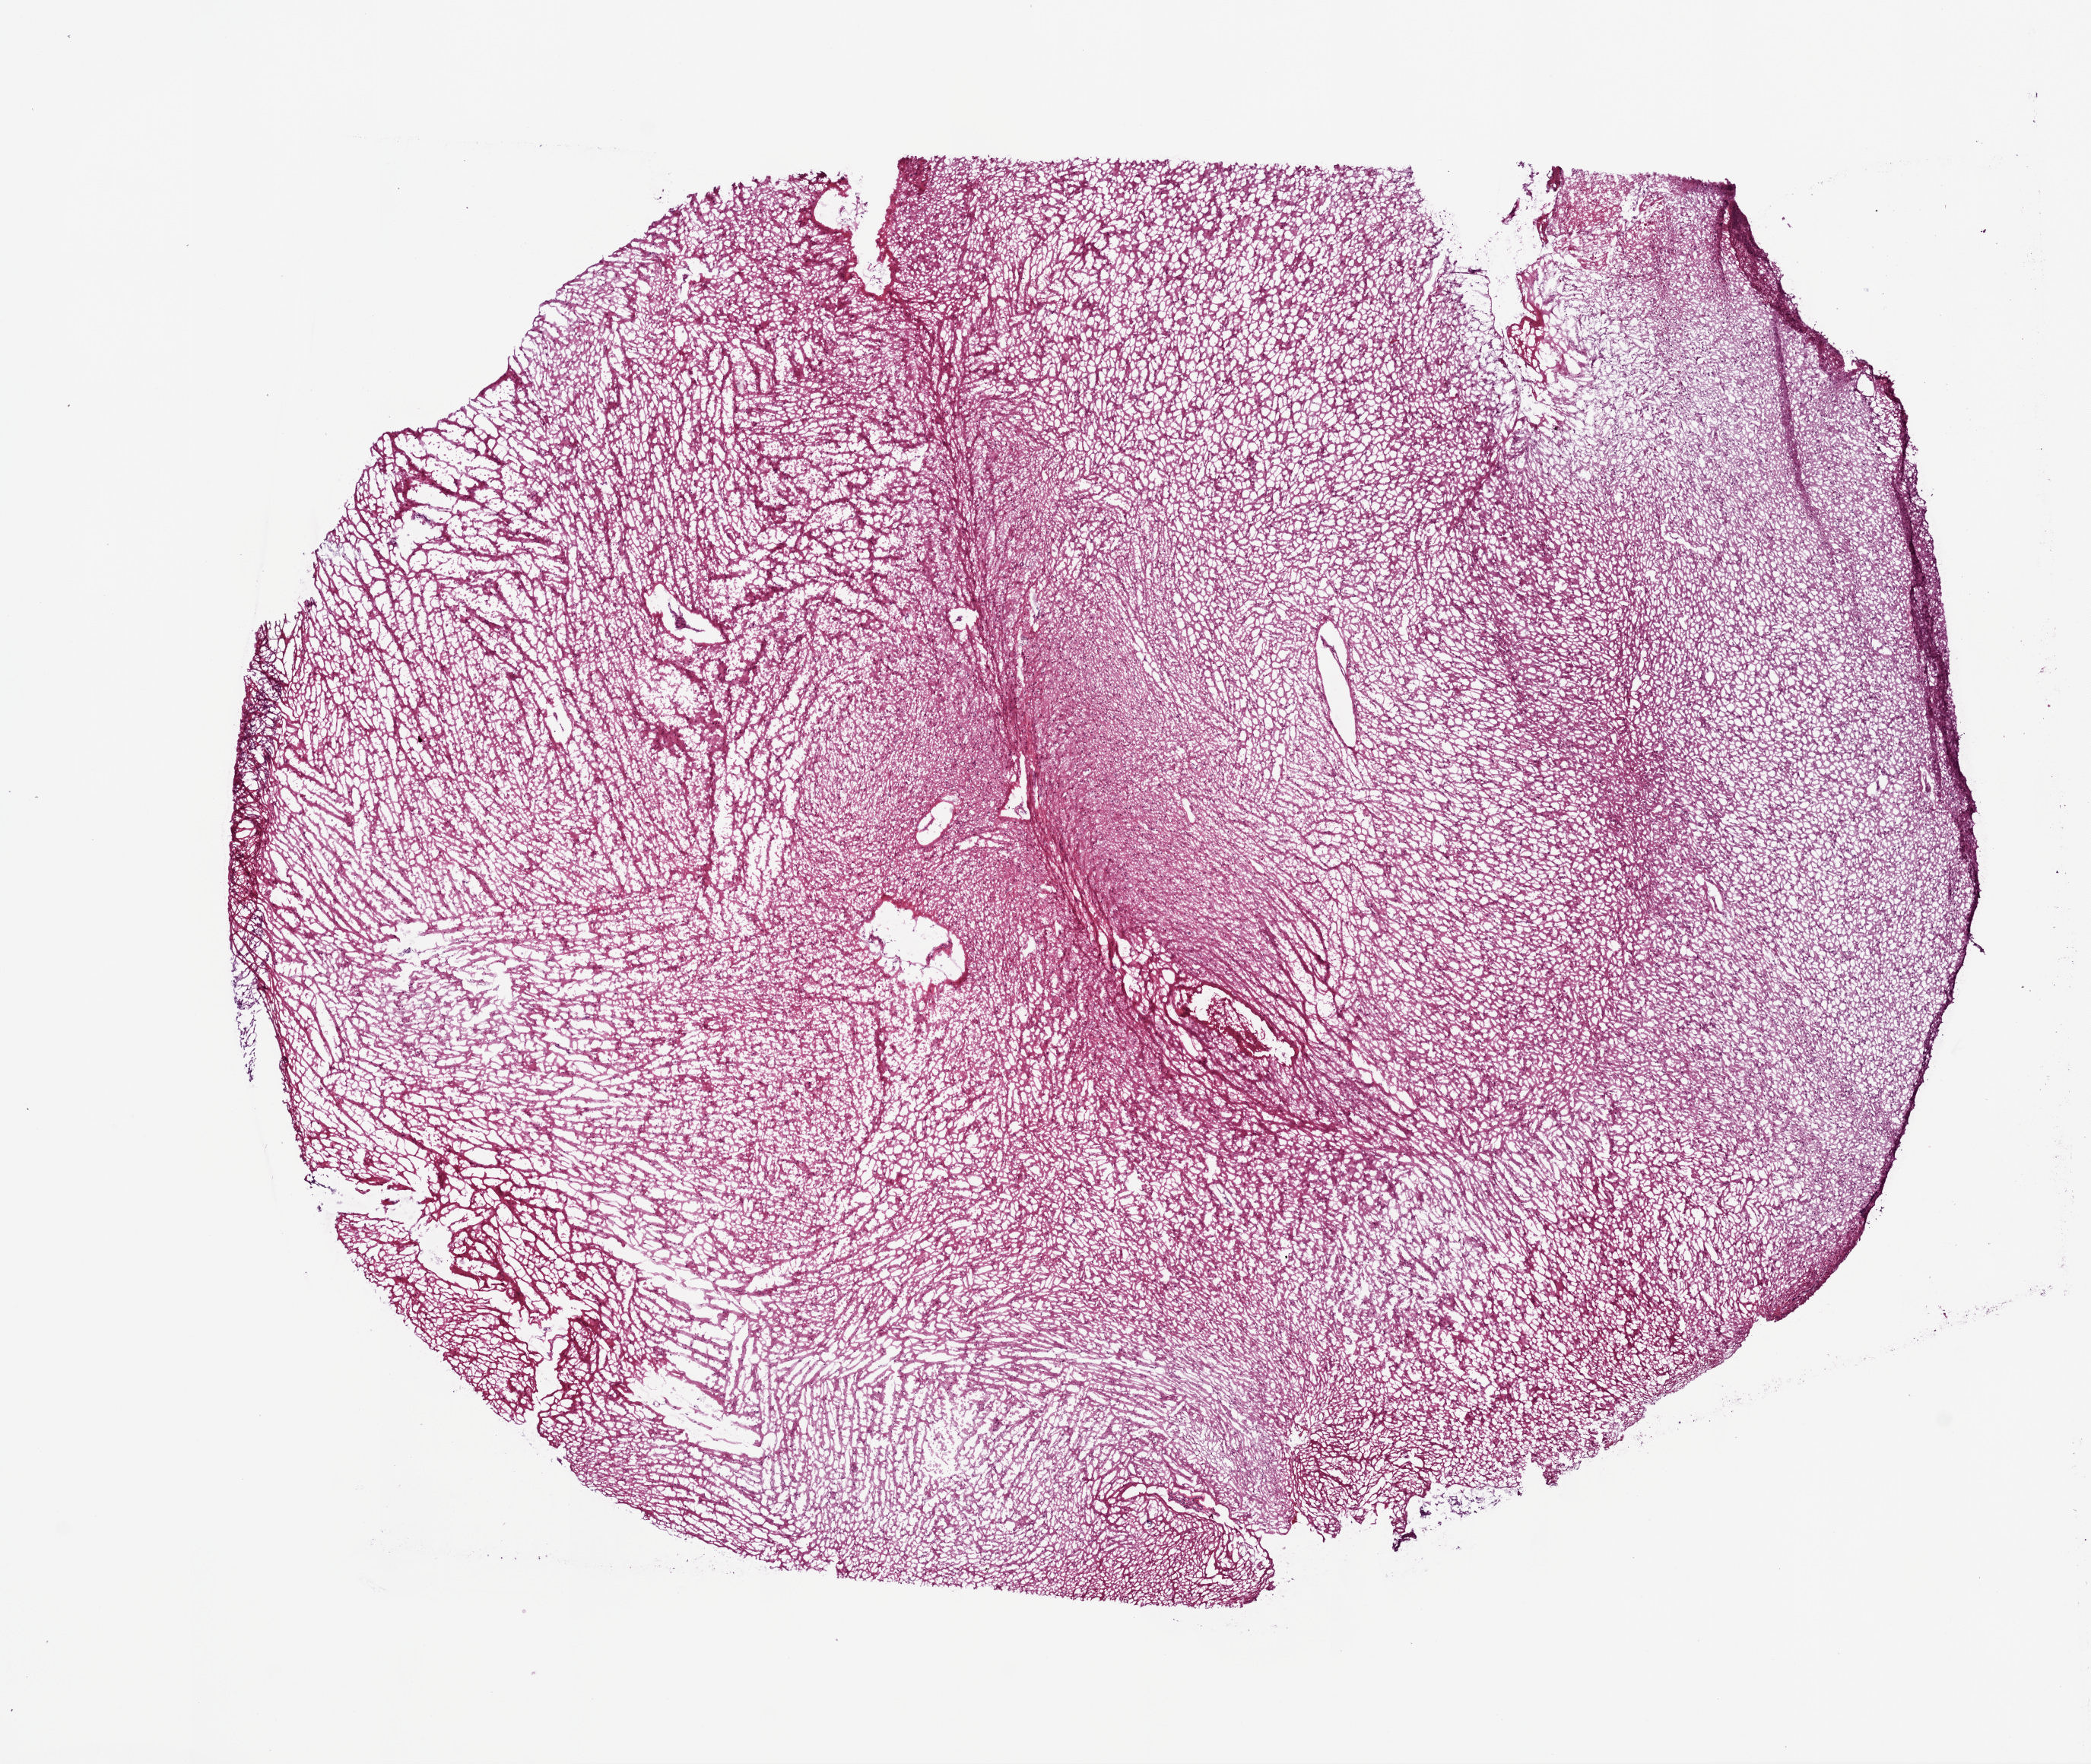
Digitized H&E-stained tissue section (whole slide) — whole scanned area (about 11.0 x 9.3 mm) shown as a low-resolution overview. Frozen section from the bottom of the tissue portion. Sample: primary tumour, brain. Male patient; age at initial diagnosis 50 years. Histologic grade: G2 (moderately differentiated). Slide review estimates, as recorded: tumour cells 100%, tumour nuclei 60%, normal cells 0%, stromal cells 0%, necrosis 0%.
Diagnosis: Astrocytoma, NOS.